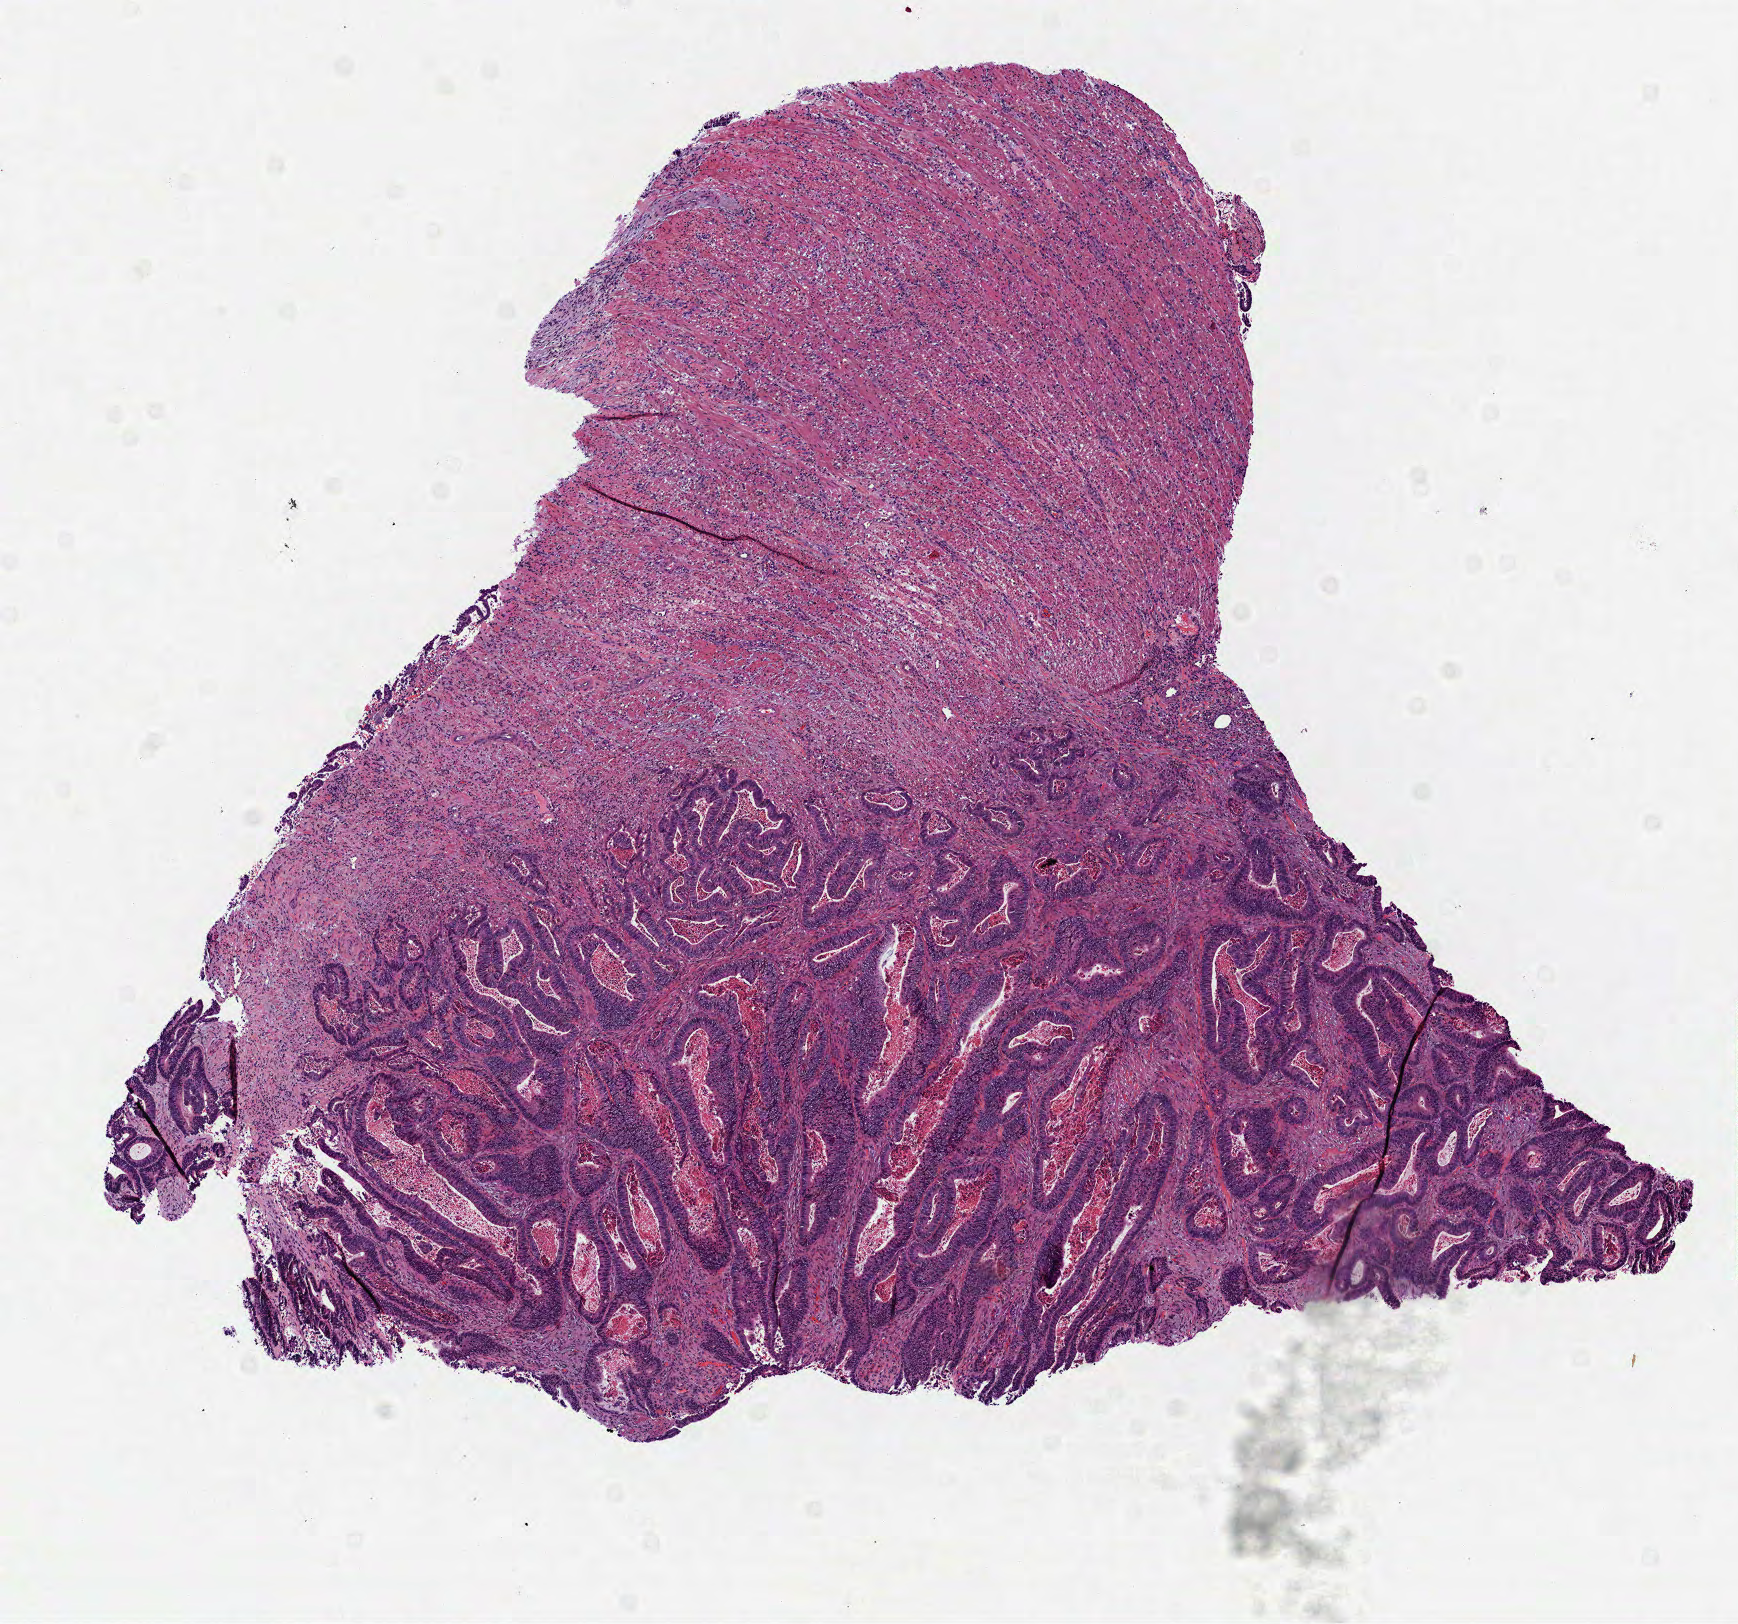
Whole-slide histology image, H&E — shown as a low-resolution overview of the whole scanned area (about 7.0 x 6.6 mm), formalin-fixed paraffin-embedded (FFPE) diagnostic section, sample: primary tumour, colon. Patient: male, age at initial diagnosis 62 years.
Histologic diagnosis: Adenocarcinoma, NOS. Lymph nodes positive (case pathology): 0 of 30 examined. AJCC pathologic stage: IIA.